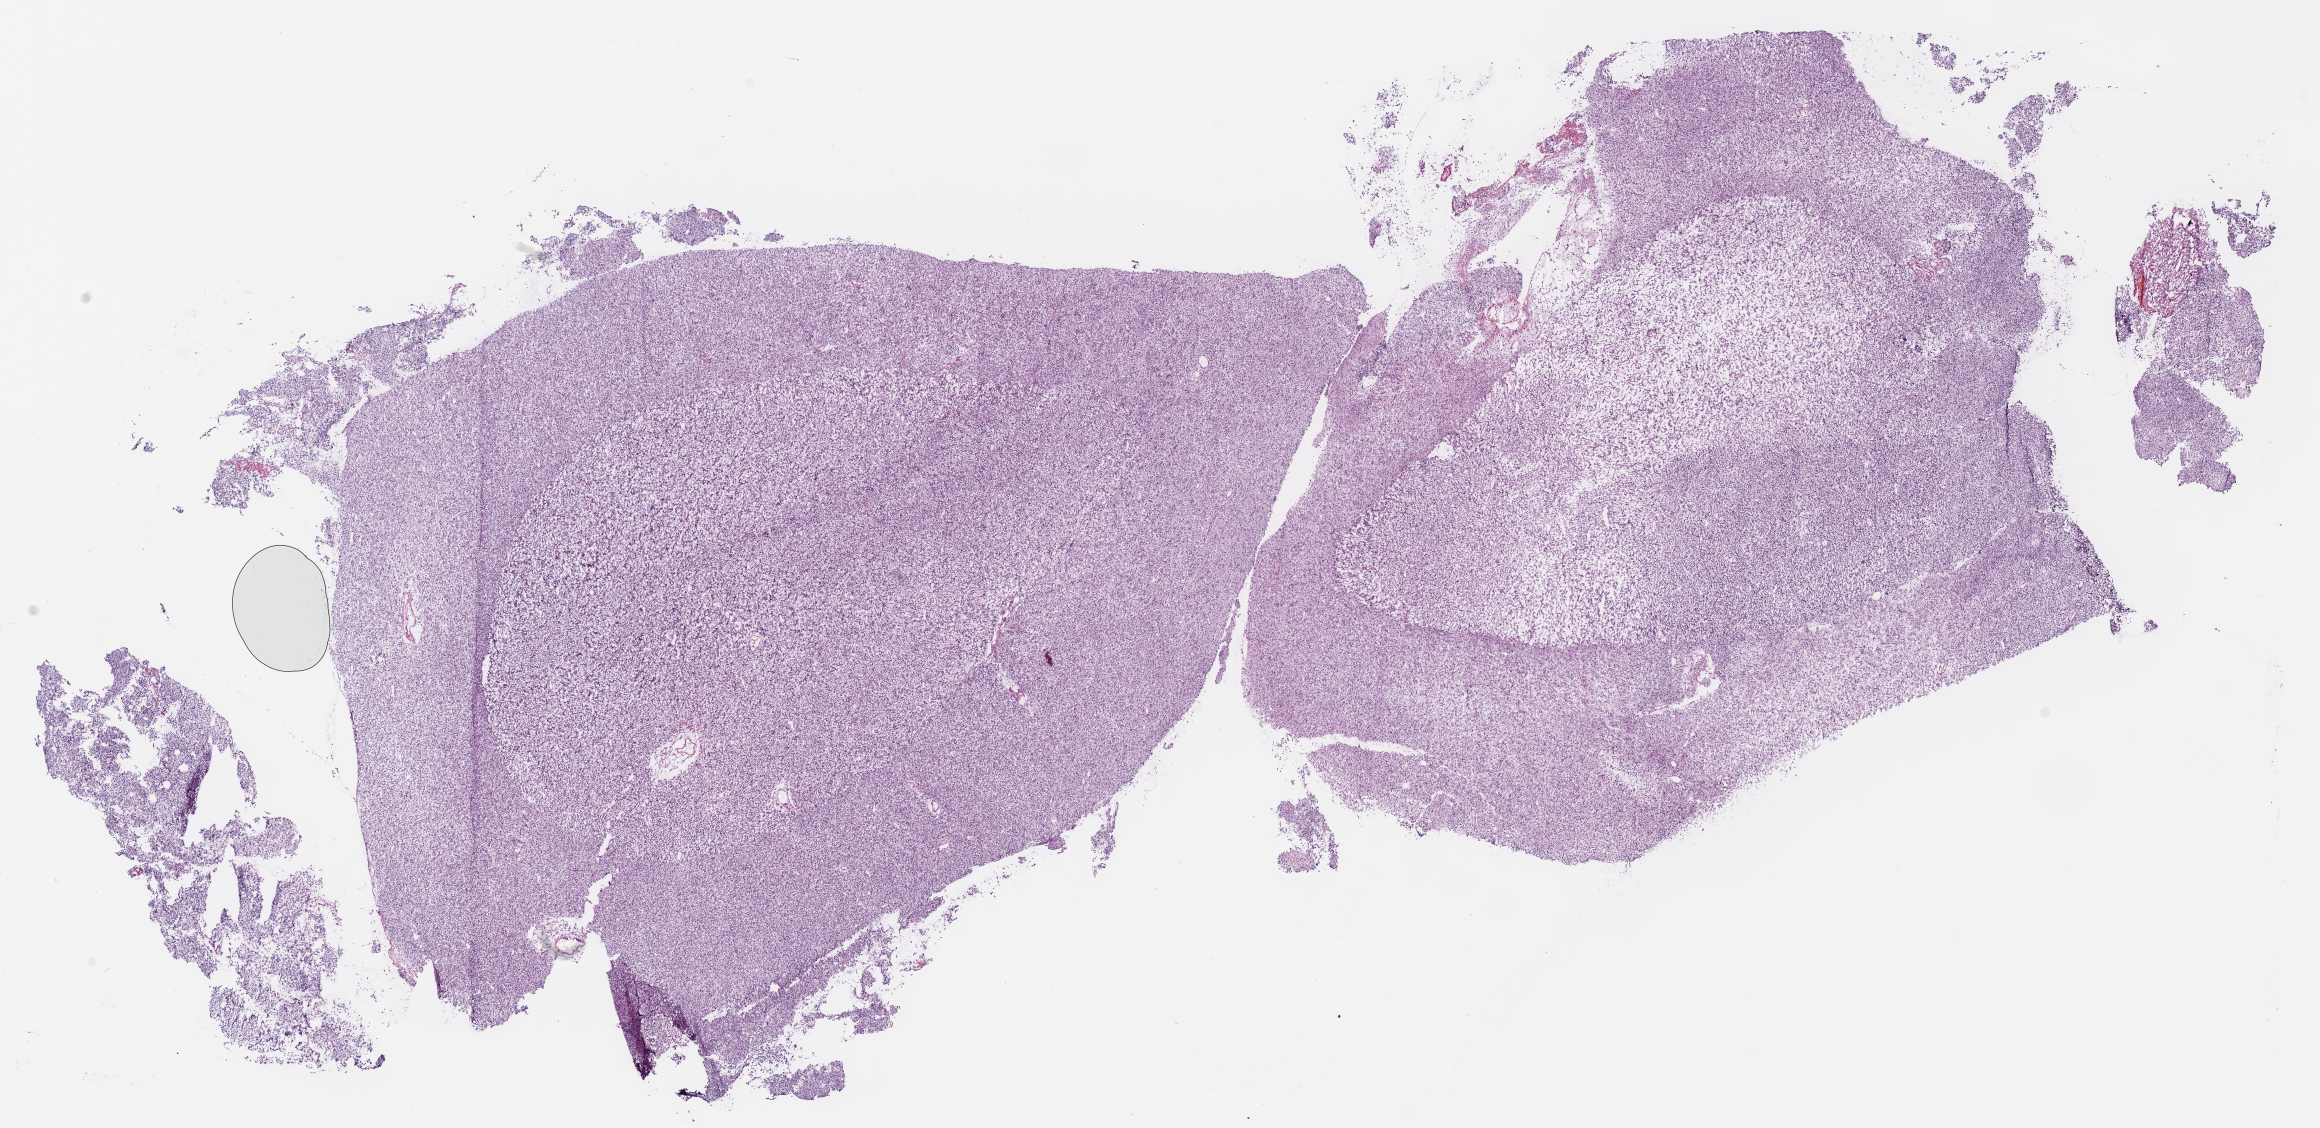
Whole-slide histology image, H&E, whole scanned area (about 18.3 x 8.9 mm) shown as a low-resolution overview; frozen section from the bottom of the tissue portion; brain, primary tumour sample. Male patient; age at initial diagnosis 30 years. Histologic grade: G3 (poorly differentiated). Slide review estimates, as recorded: tumour cells 100%, tumour nuclei 60%, normal cells 0%, stromal cells 0%, necrosis 0%.
• pathologic diagnosis: Oligodendroglioma, anaplastic (cerebrum)